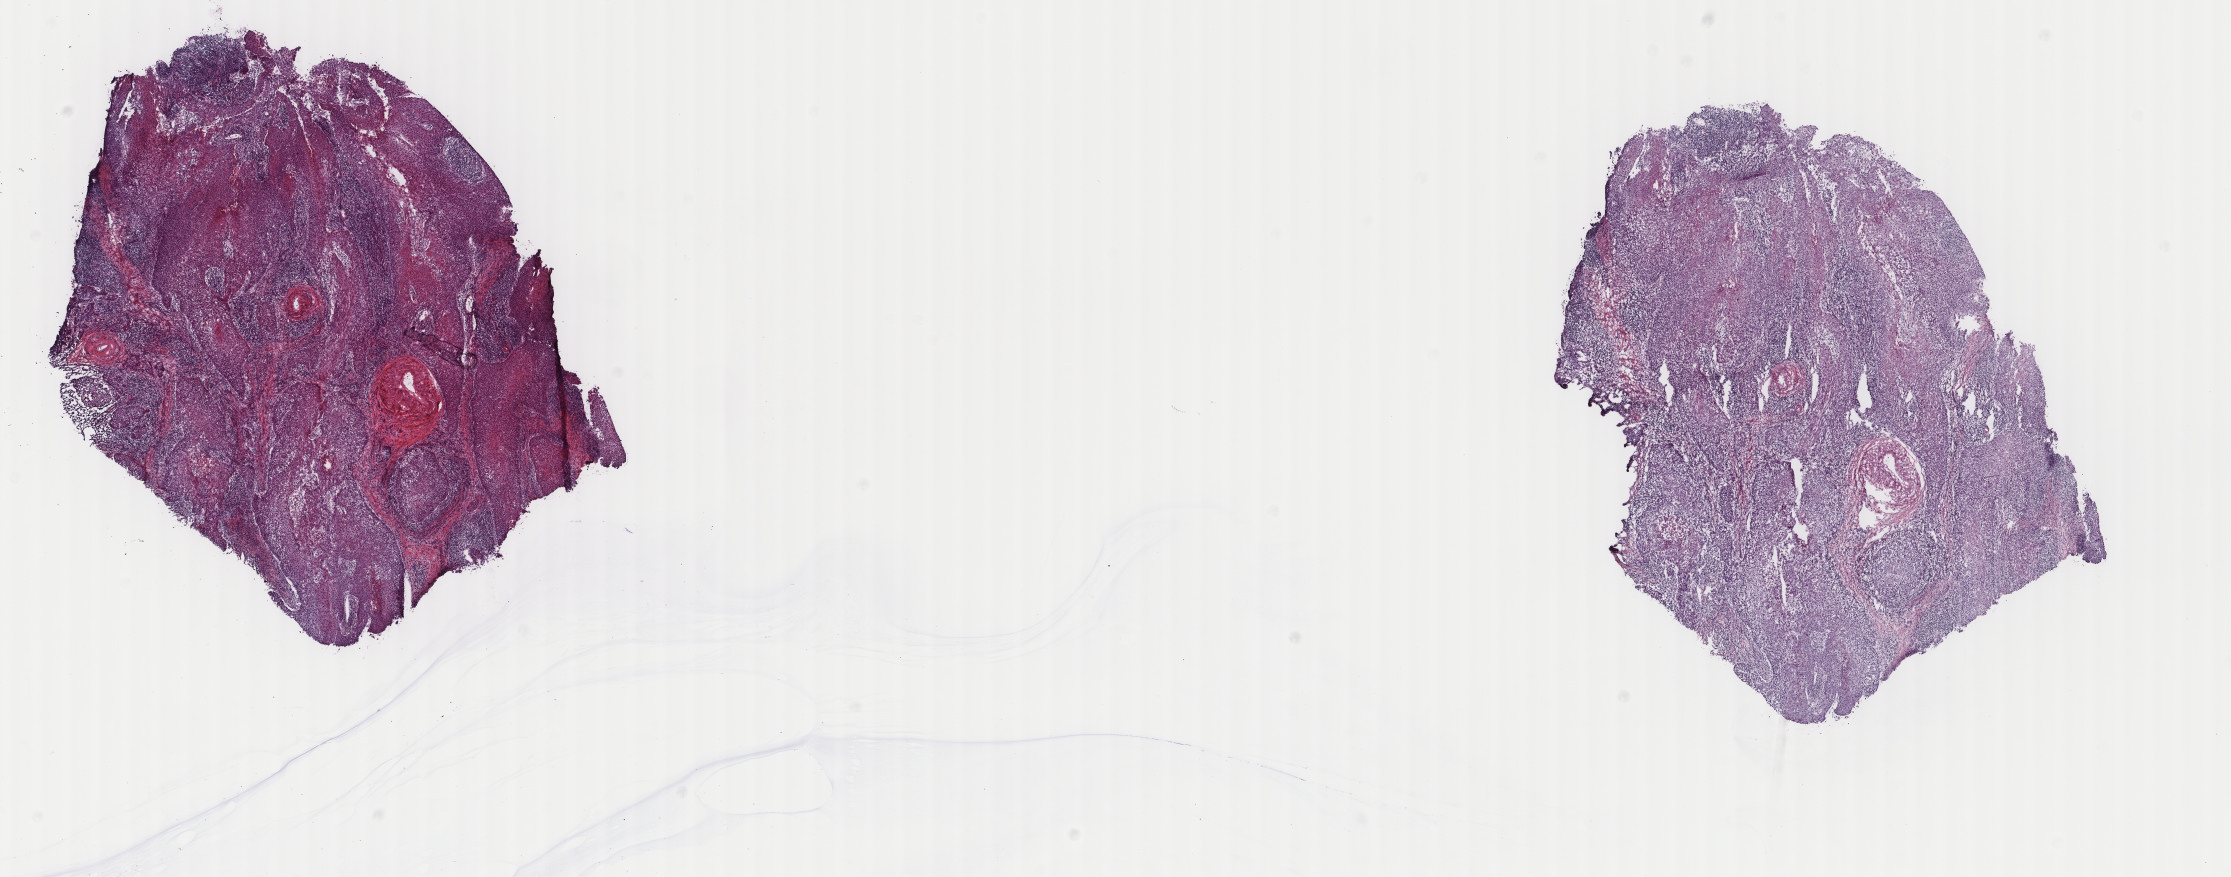
Whole-slide histology image, Hematoxylin and eosin (H&E) stained, whole scanned area (about 17.7 x 7.0 mm) shown as a low-resolution overview. Frozen section from the top of the tissue portion. Primary tumour sample from the cervix. Female, age 45 years at initial diagnosis. Histologic grade: G2 (moderately differentiated). Slide review estimates, as recorded: tumour cells 100%, tumour nuclei 80%, normal cells 0%, stromal cells 0%, necrosis 0%. Infiltration values recorded for this section: lymphocyte infiltration 15%, monocyte infiltration 0%, neutrophil infiltration 0%.
FIGO stage: IB. Histologic diagnosis: Squamous cell carcinoma, large cell, nonkeratinizing, NOS.